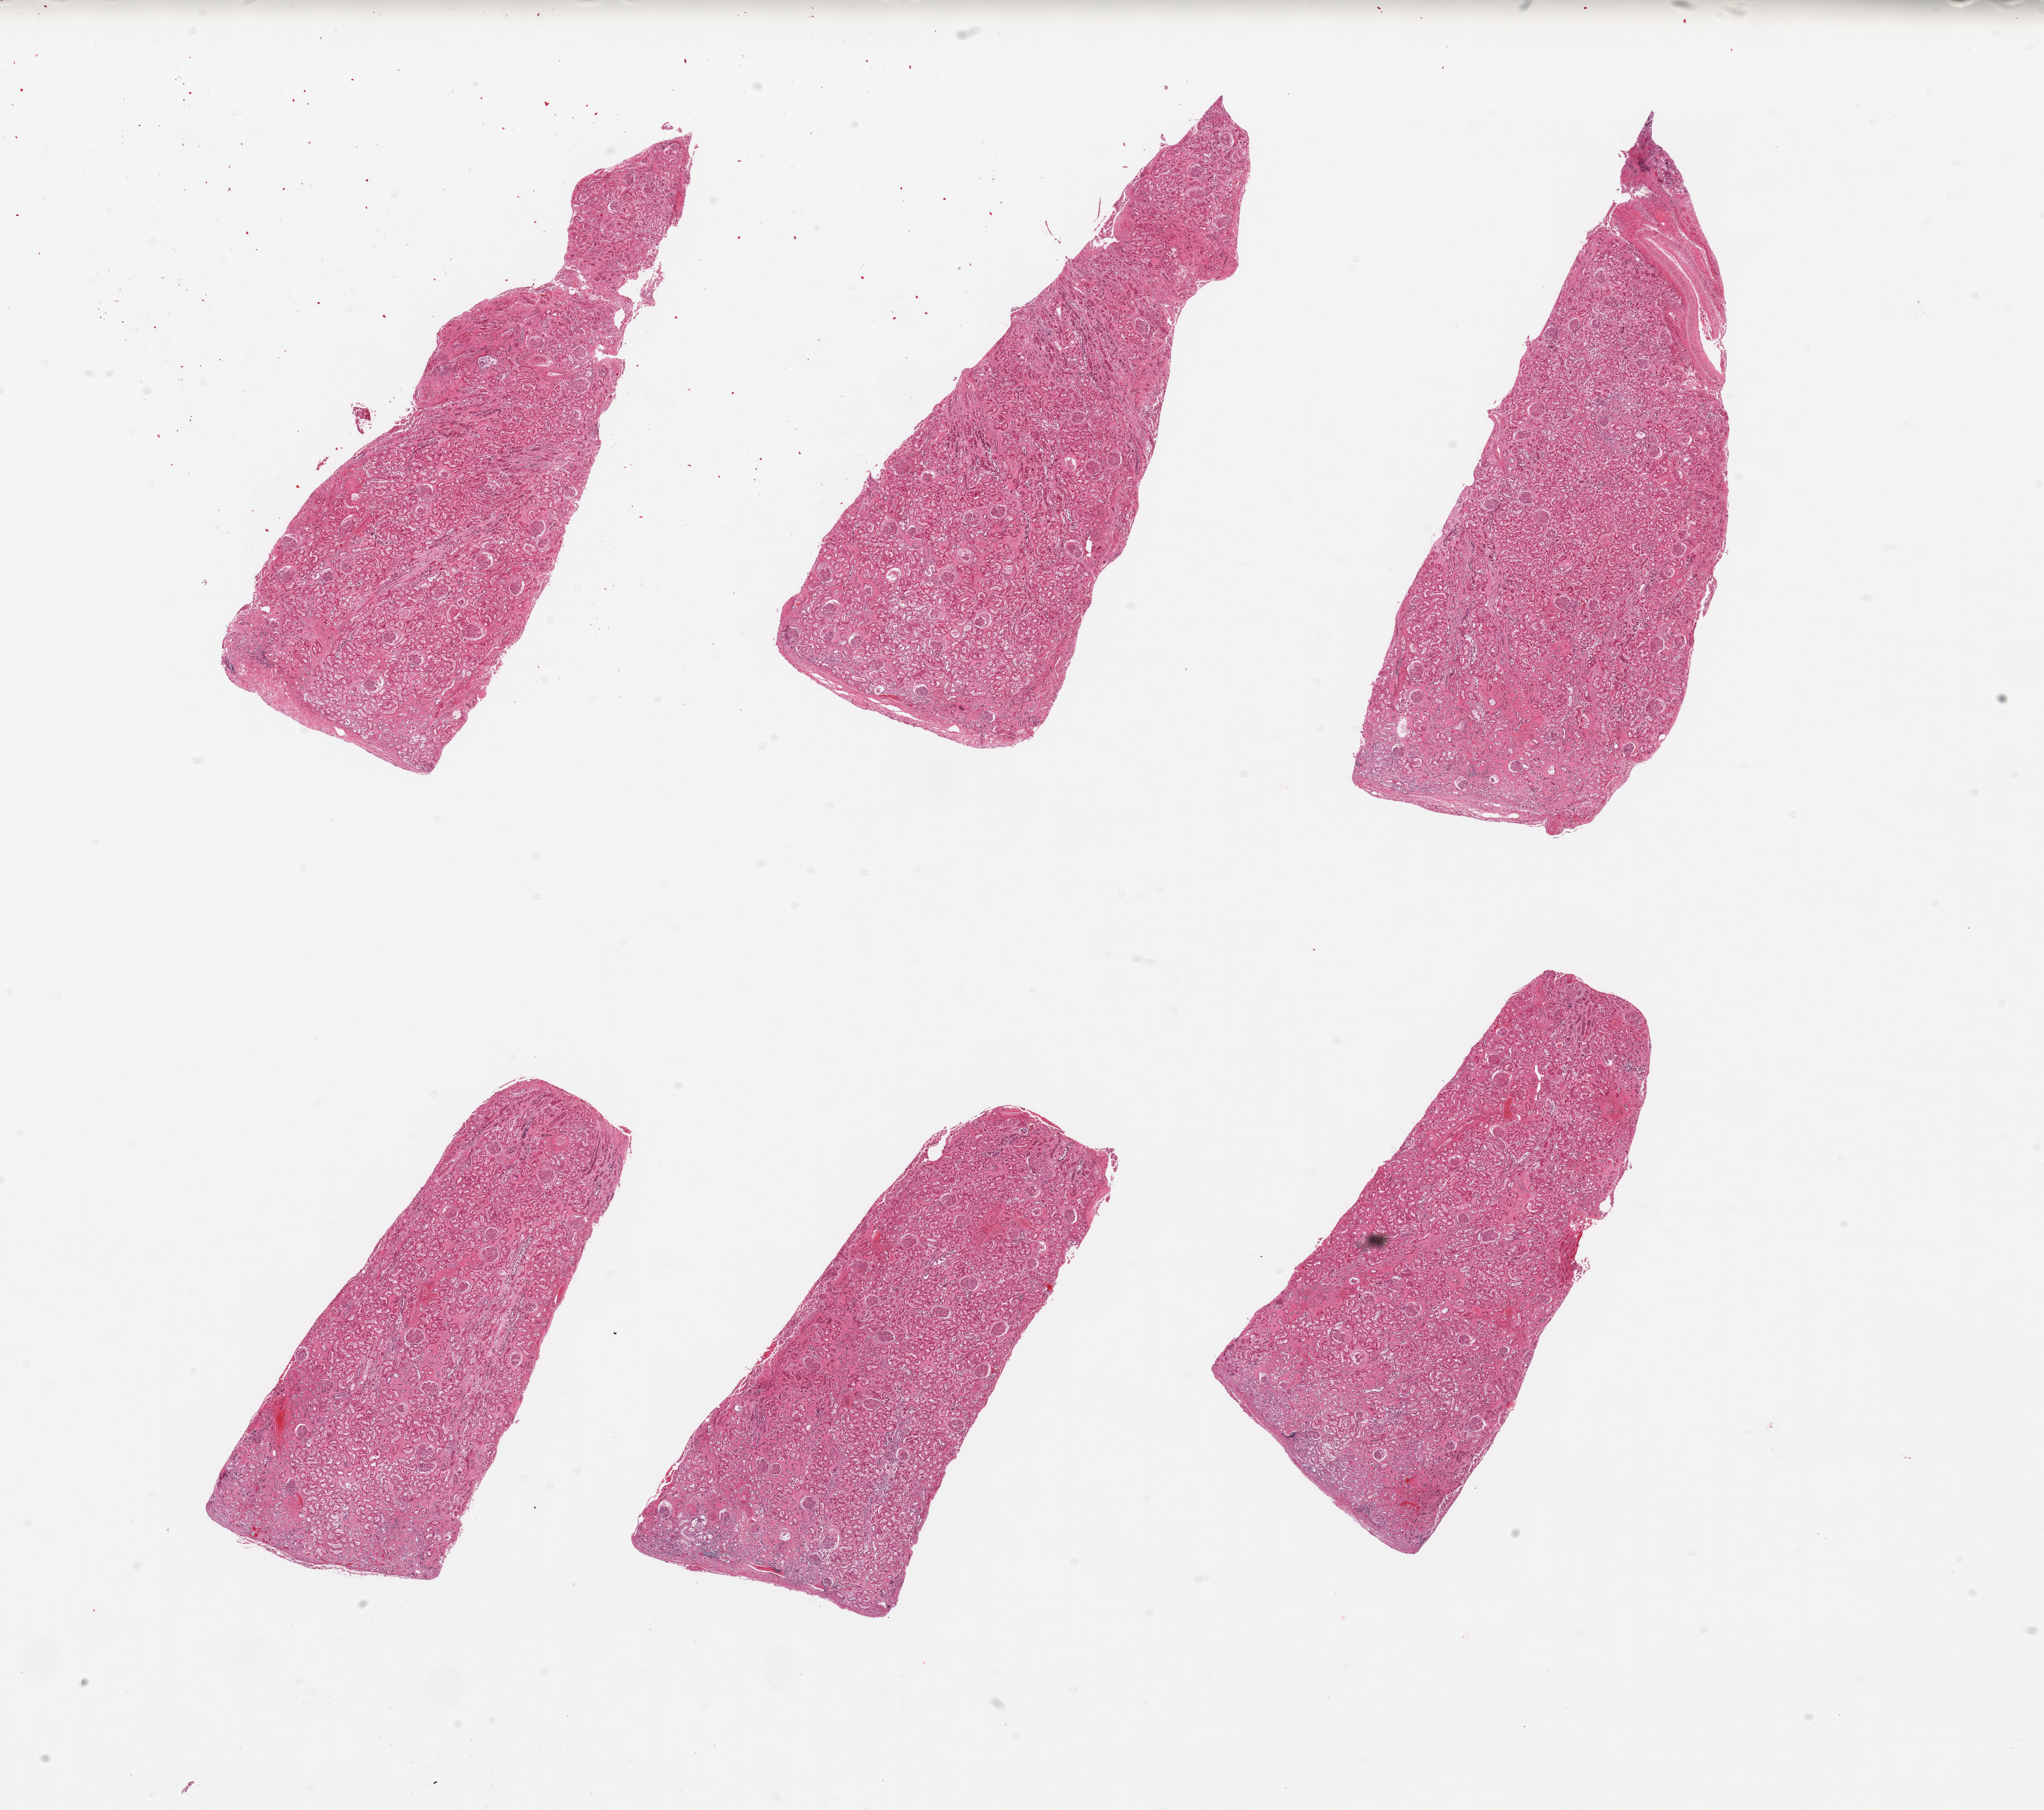
Whole-slide image, hematoxylin and eosin (H&E) stain, shown as a low-resolution overview of the whole scanned area (about 24.6 x 21.8 mm), PAXgene-fixed paraffin-embedded (PFPE) section, target tissue: renal cortex, tissue donor sample.
* review note (as recorded): 6 pieces; mild to moderate autolysis; interstitial fibrosis and scarring; rare sclerosed glomeruli; one piece contains at the tip large vessel walls